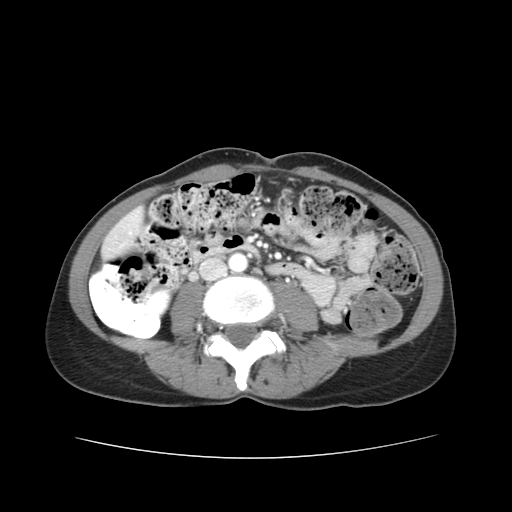
Contrast-enhanced abdominal CT, one axial slice; slice 5 of 38 in the series (ordered by position); 120 kVp; intravenous contrast given; soft-tissue window (W 400 / L 40 HU); 5 mm slice thickness; 512 × 512 image matrix, field of view 340 × 340 mm. Female patient, age 54 years. From the clinical record (not read from this slice): diagnosis: colorectal cancer liver metastases, imaged before liver resection; multiple liver metastases: yes; largest metastasis: 1.1 cm; chemotherapy before resection: yes.
Outlined on this slice (expert manual segmentation):
- liver: bounding box <106,215,141,254> (left, top, right, bottom; pixels)